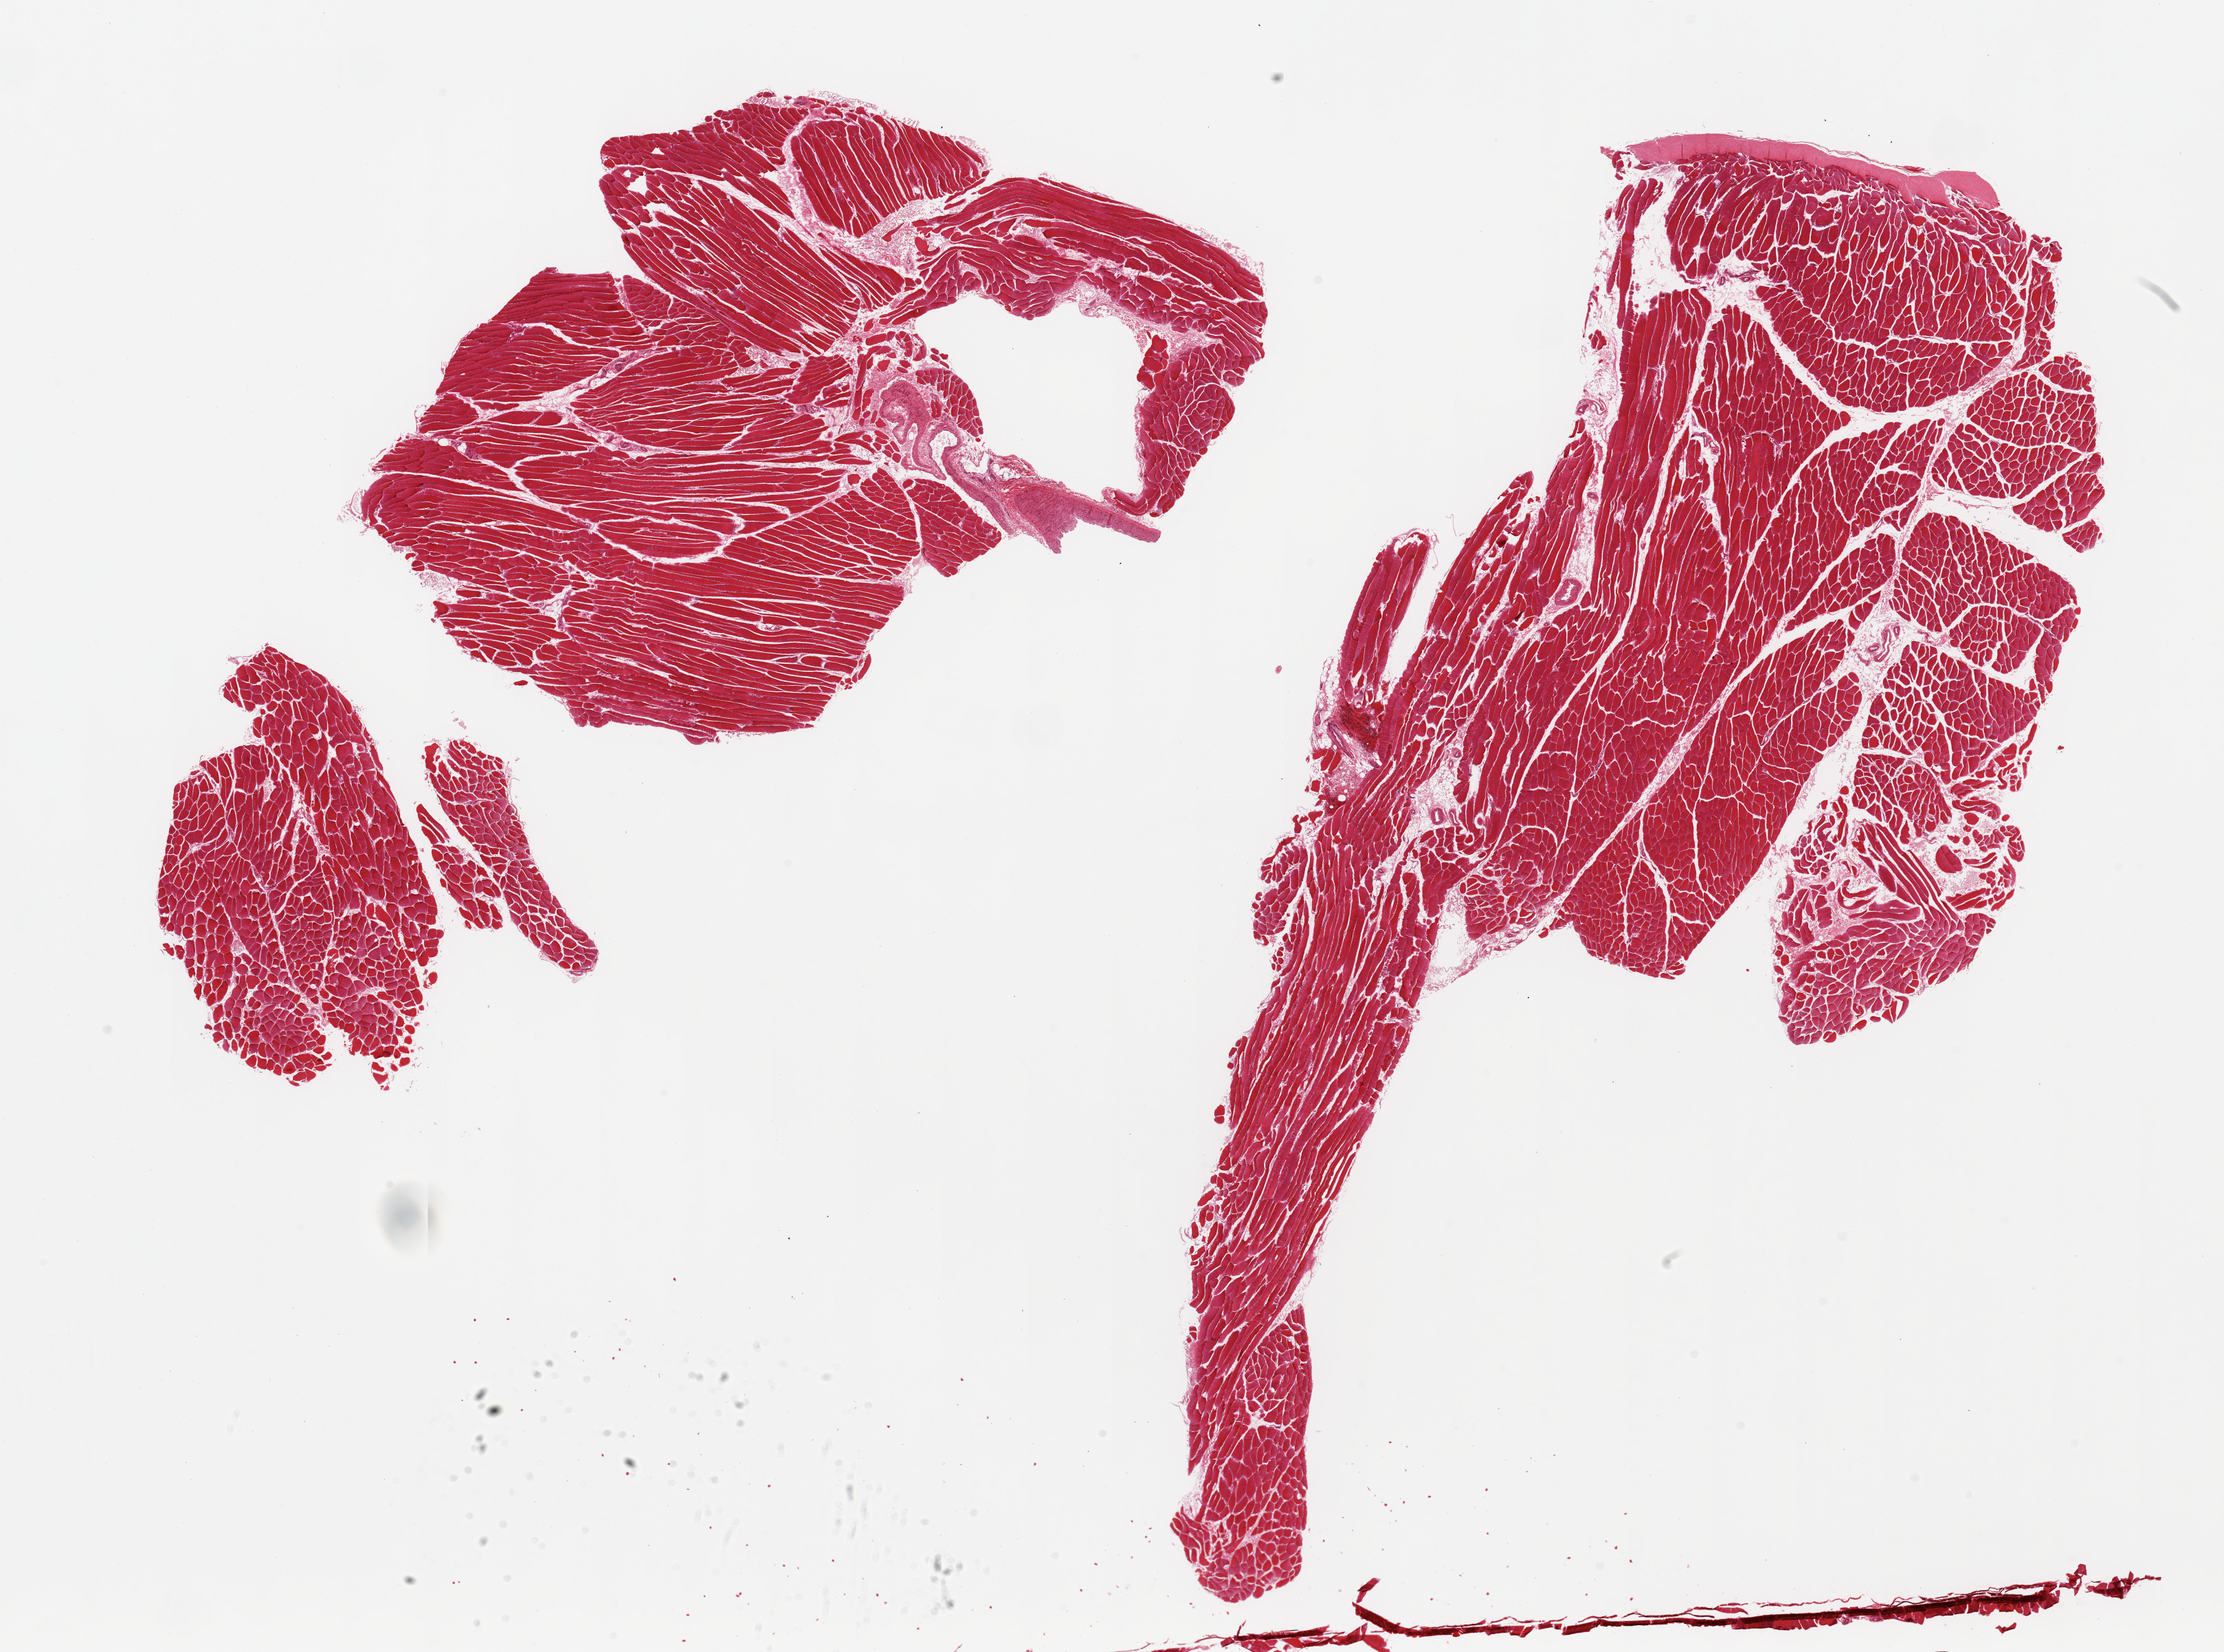
Whole-slide image, hematoxylin and eosin (H&E) stain, brightfield, whole scanned area (about 25.6 x 19.0 mm, acquisition: 20x scan) shown as a low-resolution overview, PAXgene-fixed, paraffin-embedded tissue, target tissue: skeletal muscle, donor tissue sample. Donor: male.
• pathologist's review note for this sample: 2 pieces, interstitial fat/vascular elements are ~10%